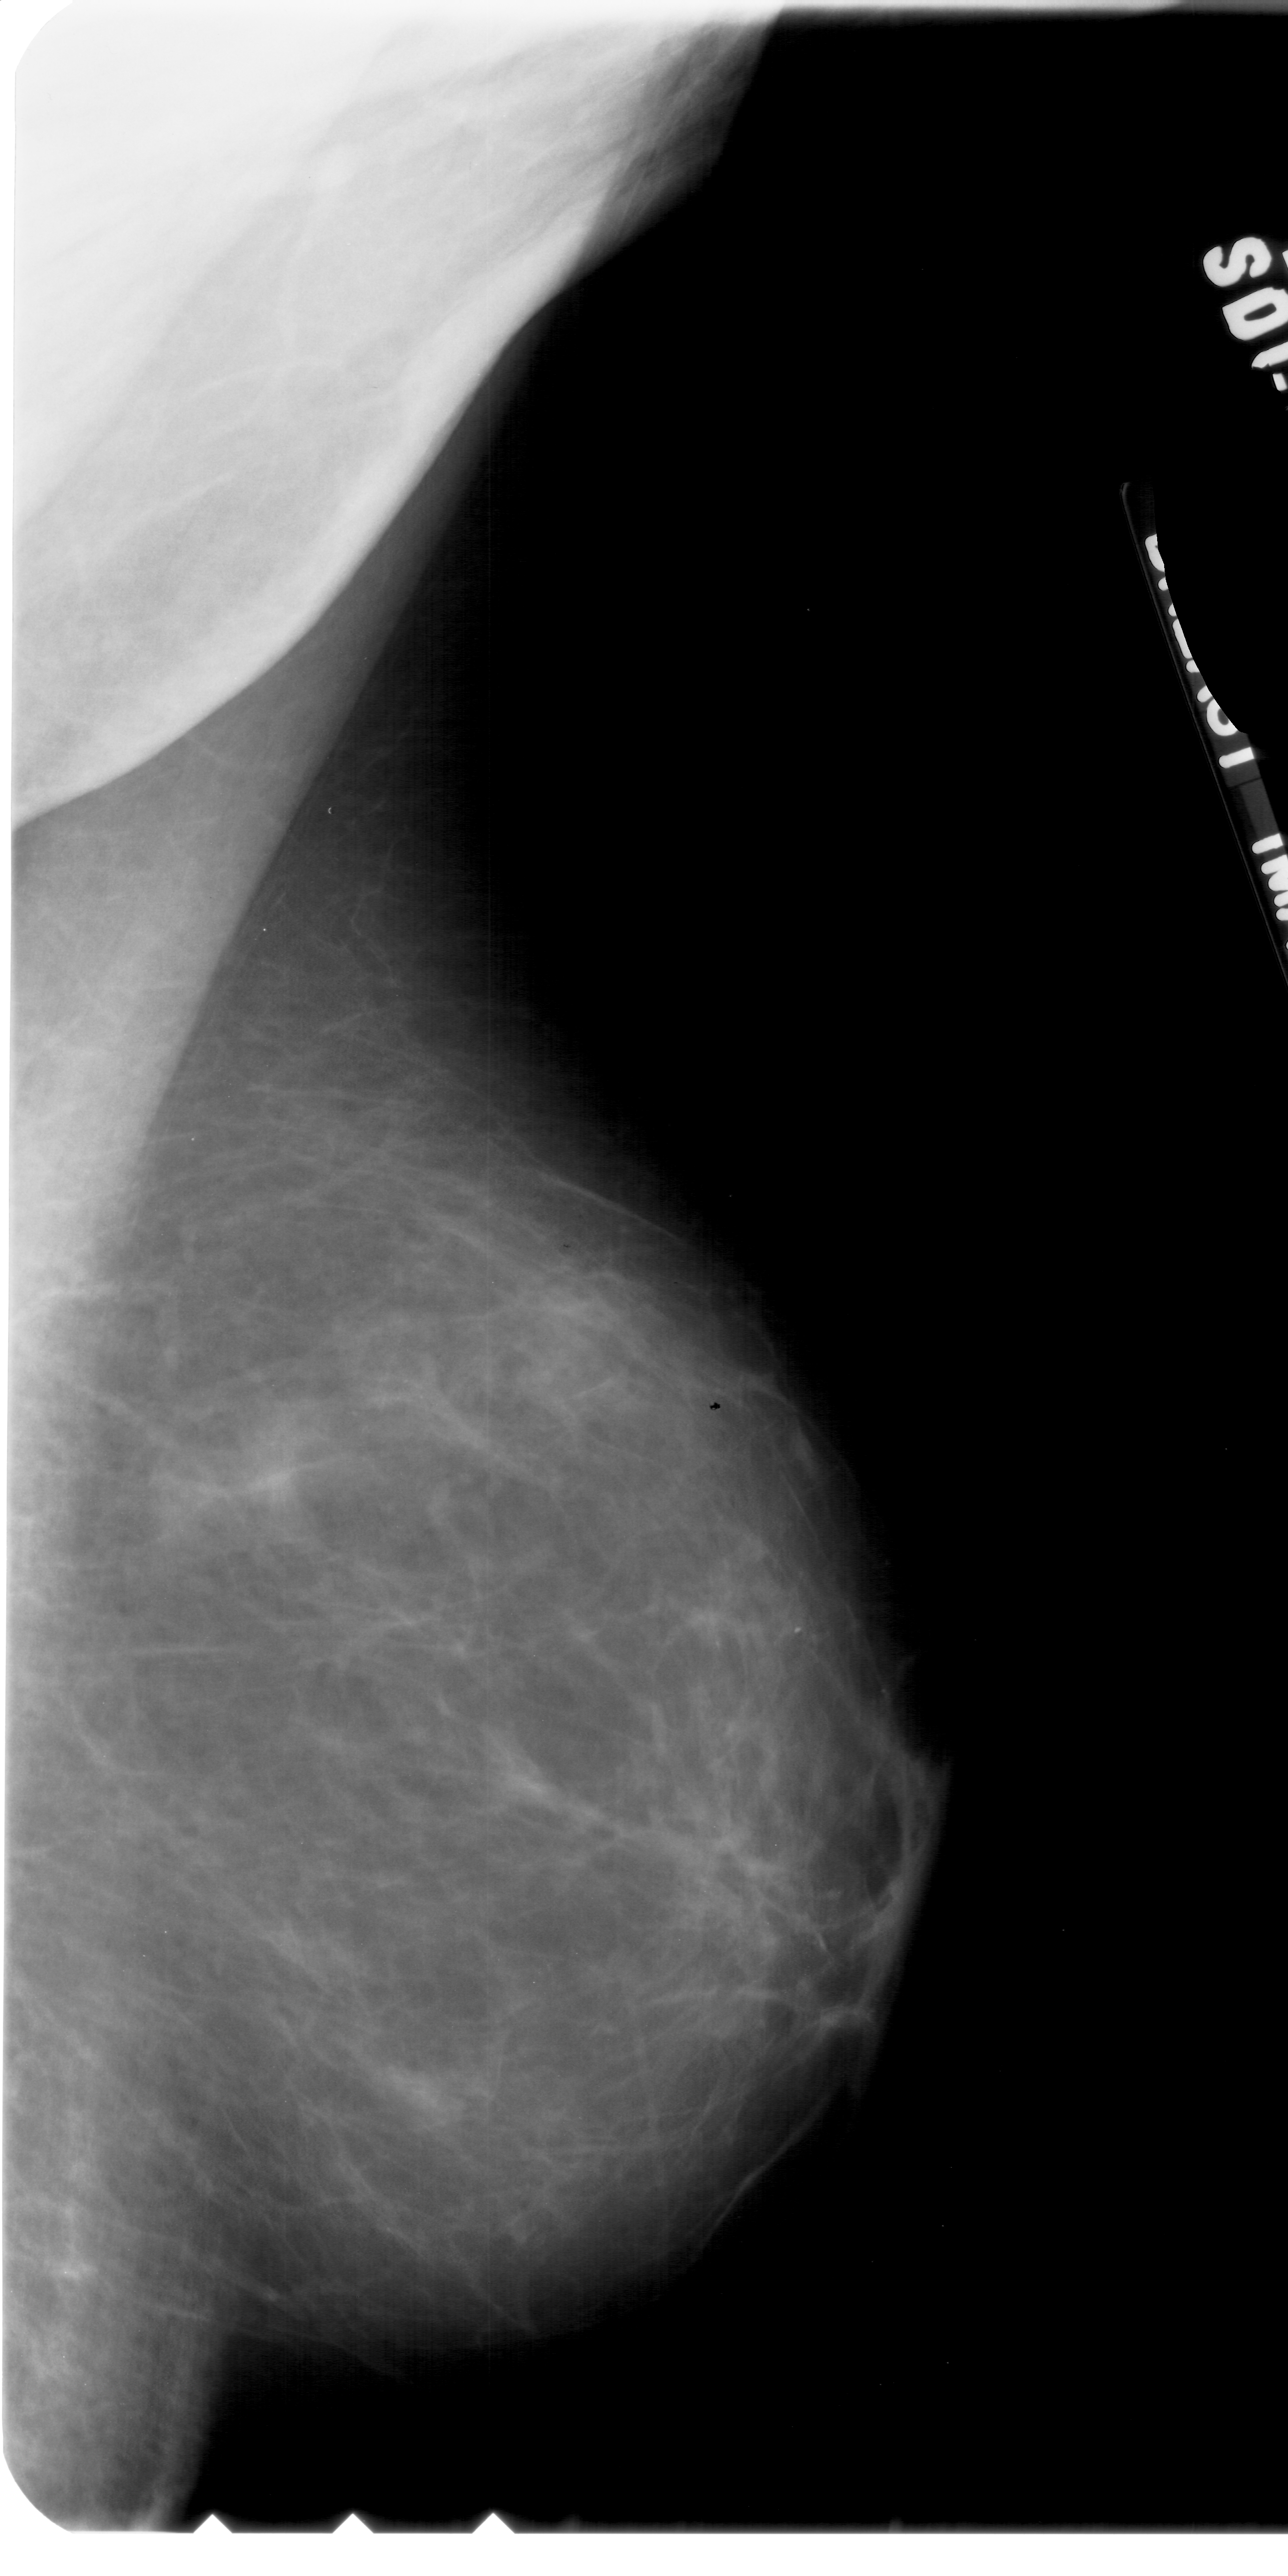
Mammogram (digitized film). Right breast. Mediolateral oblique (MLO) view. Breast composition: scattered fibroglandular densities (BI-RADS density category 2 of 4). 1288 × 2576 image matrix.
Expert-marked regions of interest on this film, with their recorded descriptors:
- calcifications, morphology pleomorphic, distribution clustered; BI-RADS assessment category 4; pathology result (as recorded, not read from the image): benign: box from (x=358, y=1330) to (x=487, y=1444) px